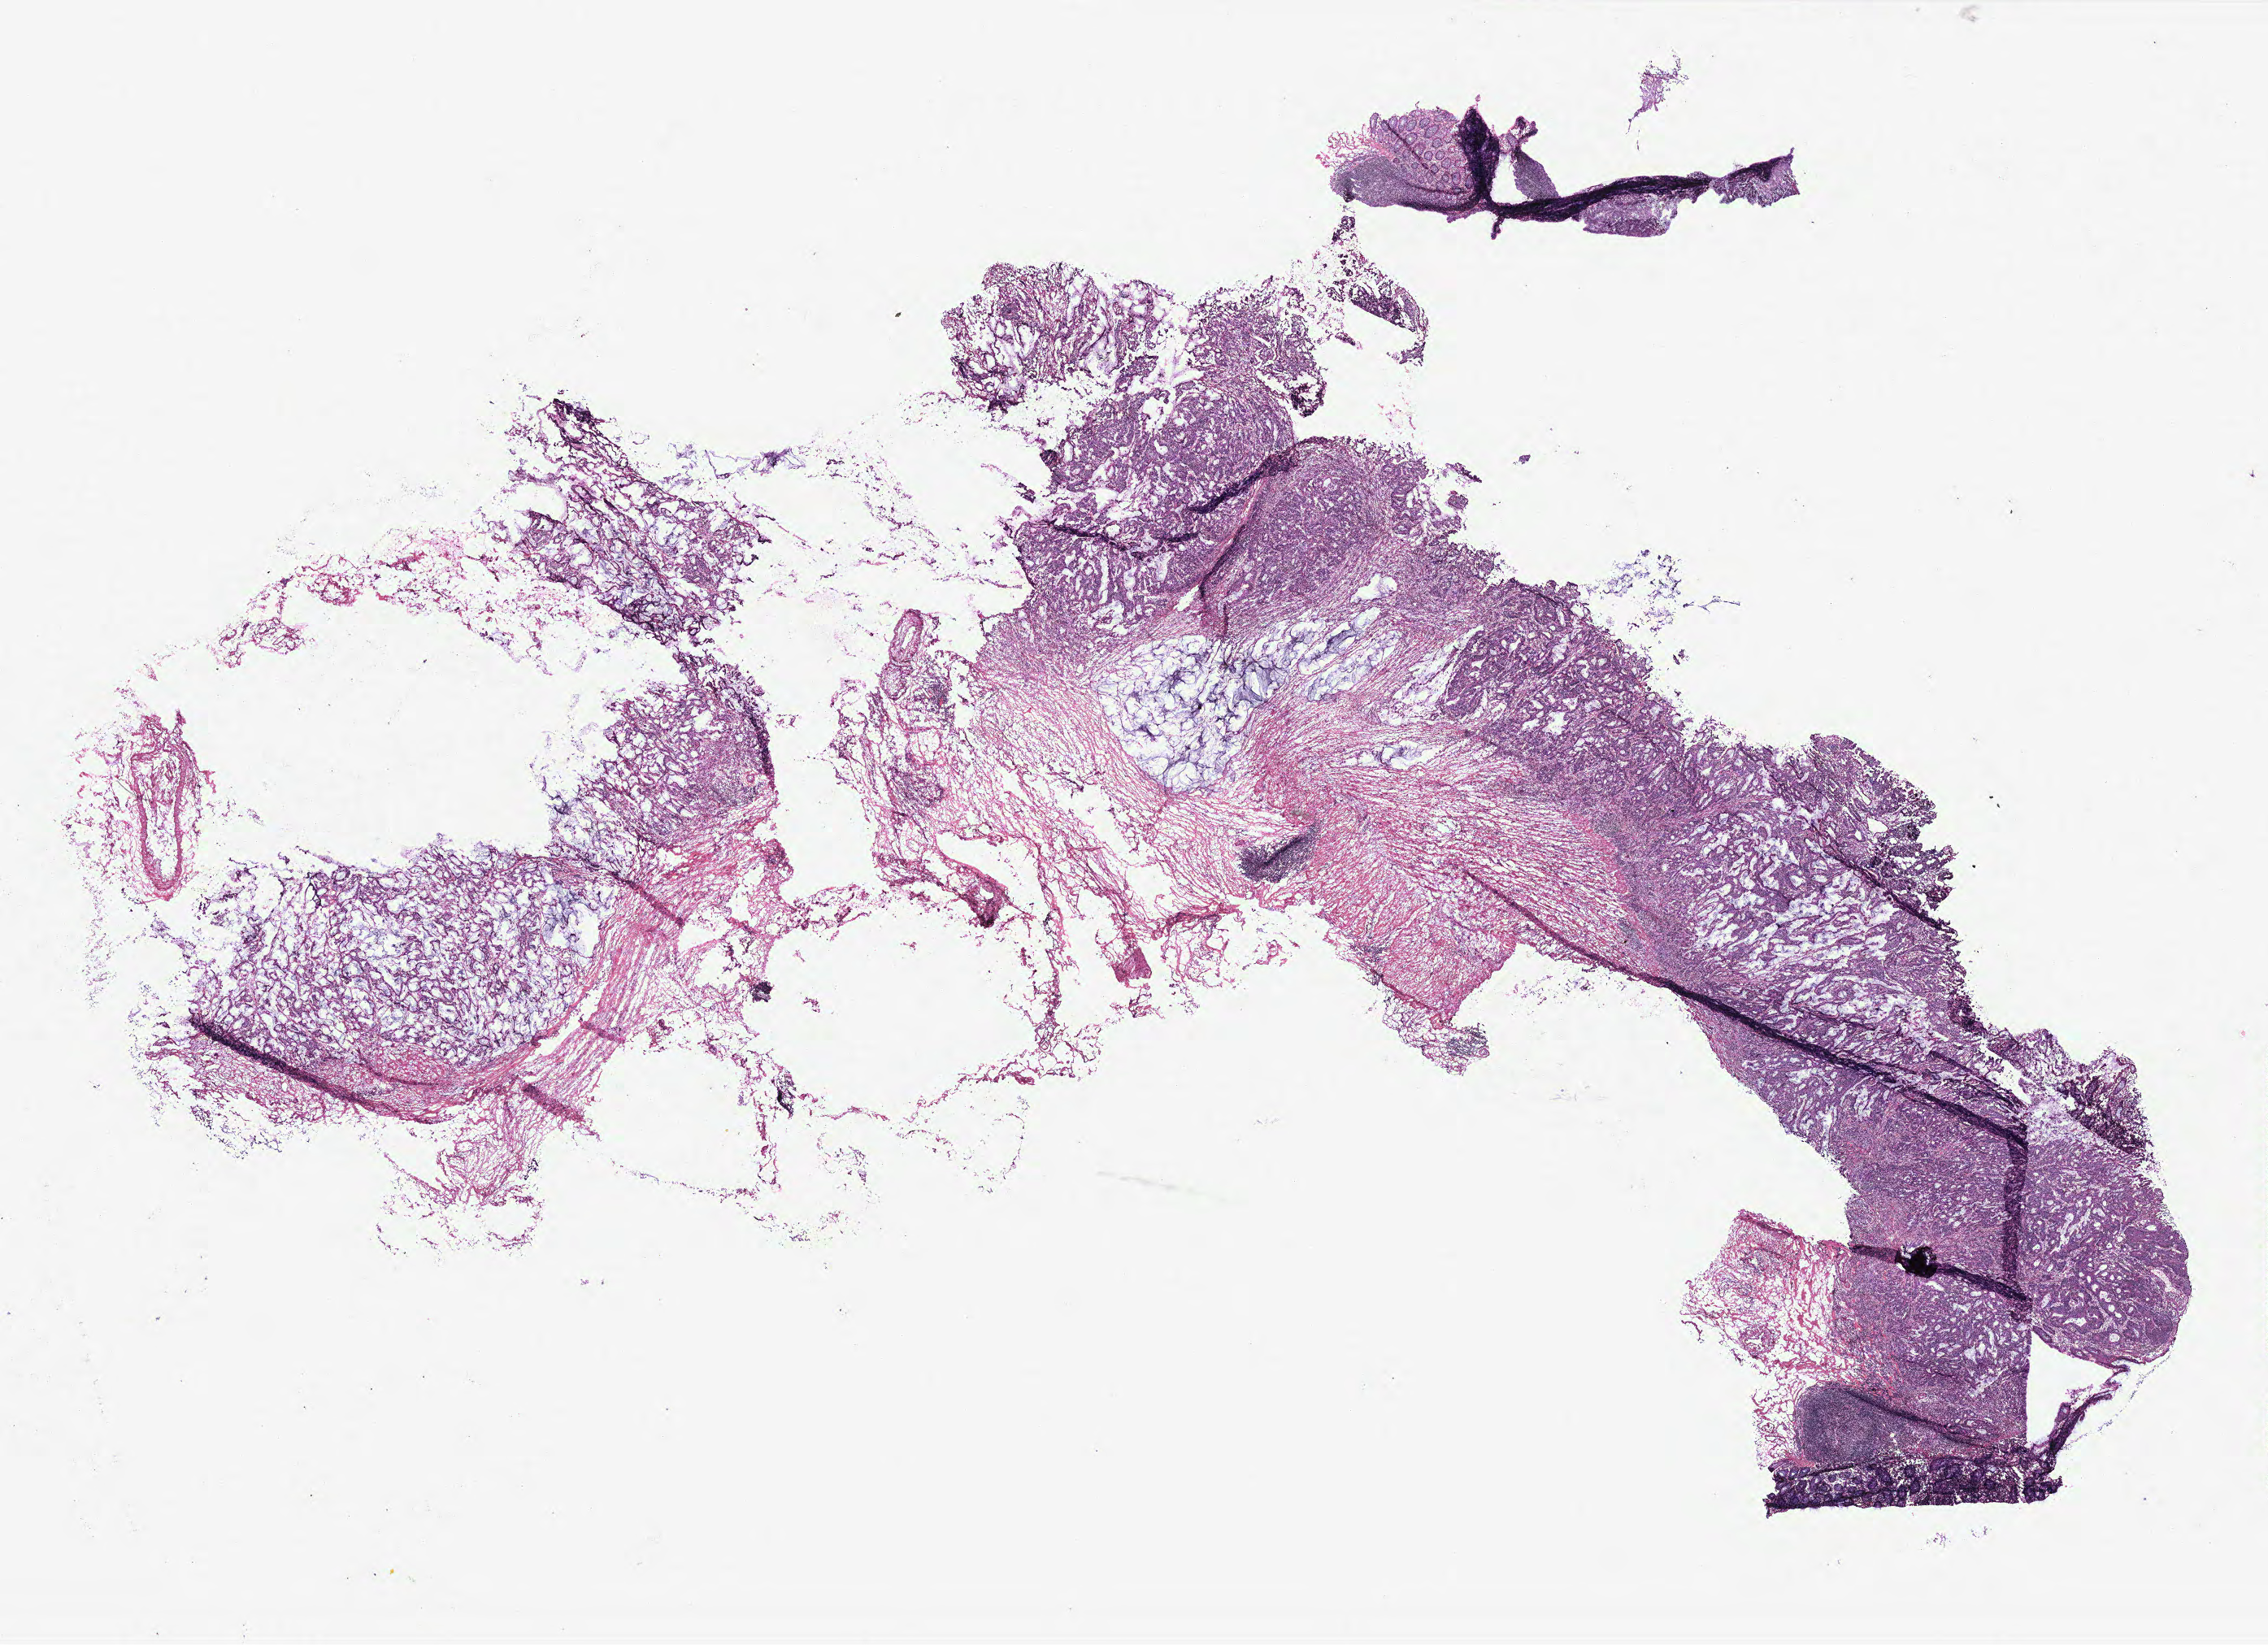
H&E whole-slide image, a low-resolution overview of the entire scanned area, about 22.3 x 16.2 mm (acquisition: 40x scan), colon, normal (non-tumour) tissue. Patient: female, age 61 years.
This section: normal (non-tumour) tissue from the same patient. Patient diagnosis: Adenocarcinoma, NOS.